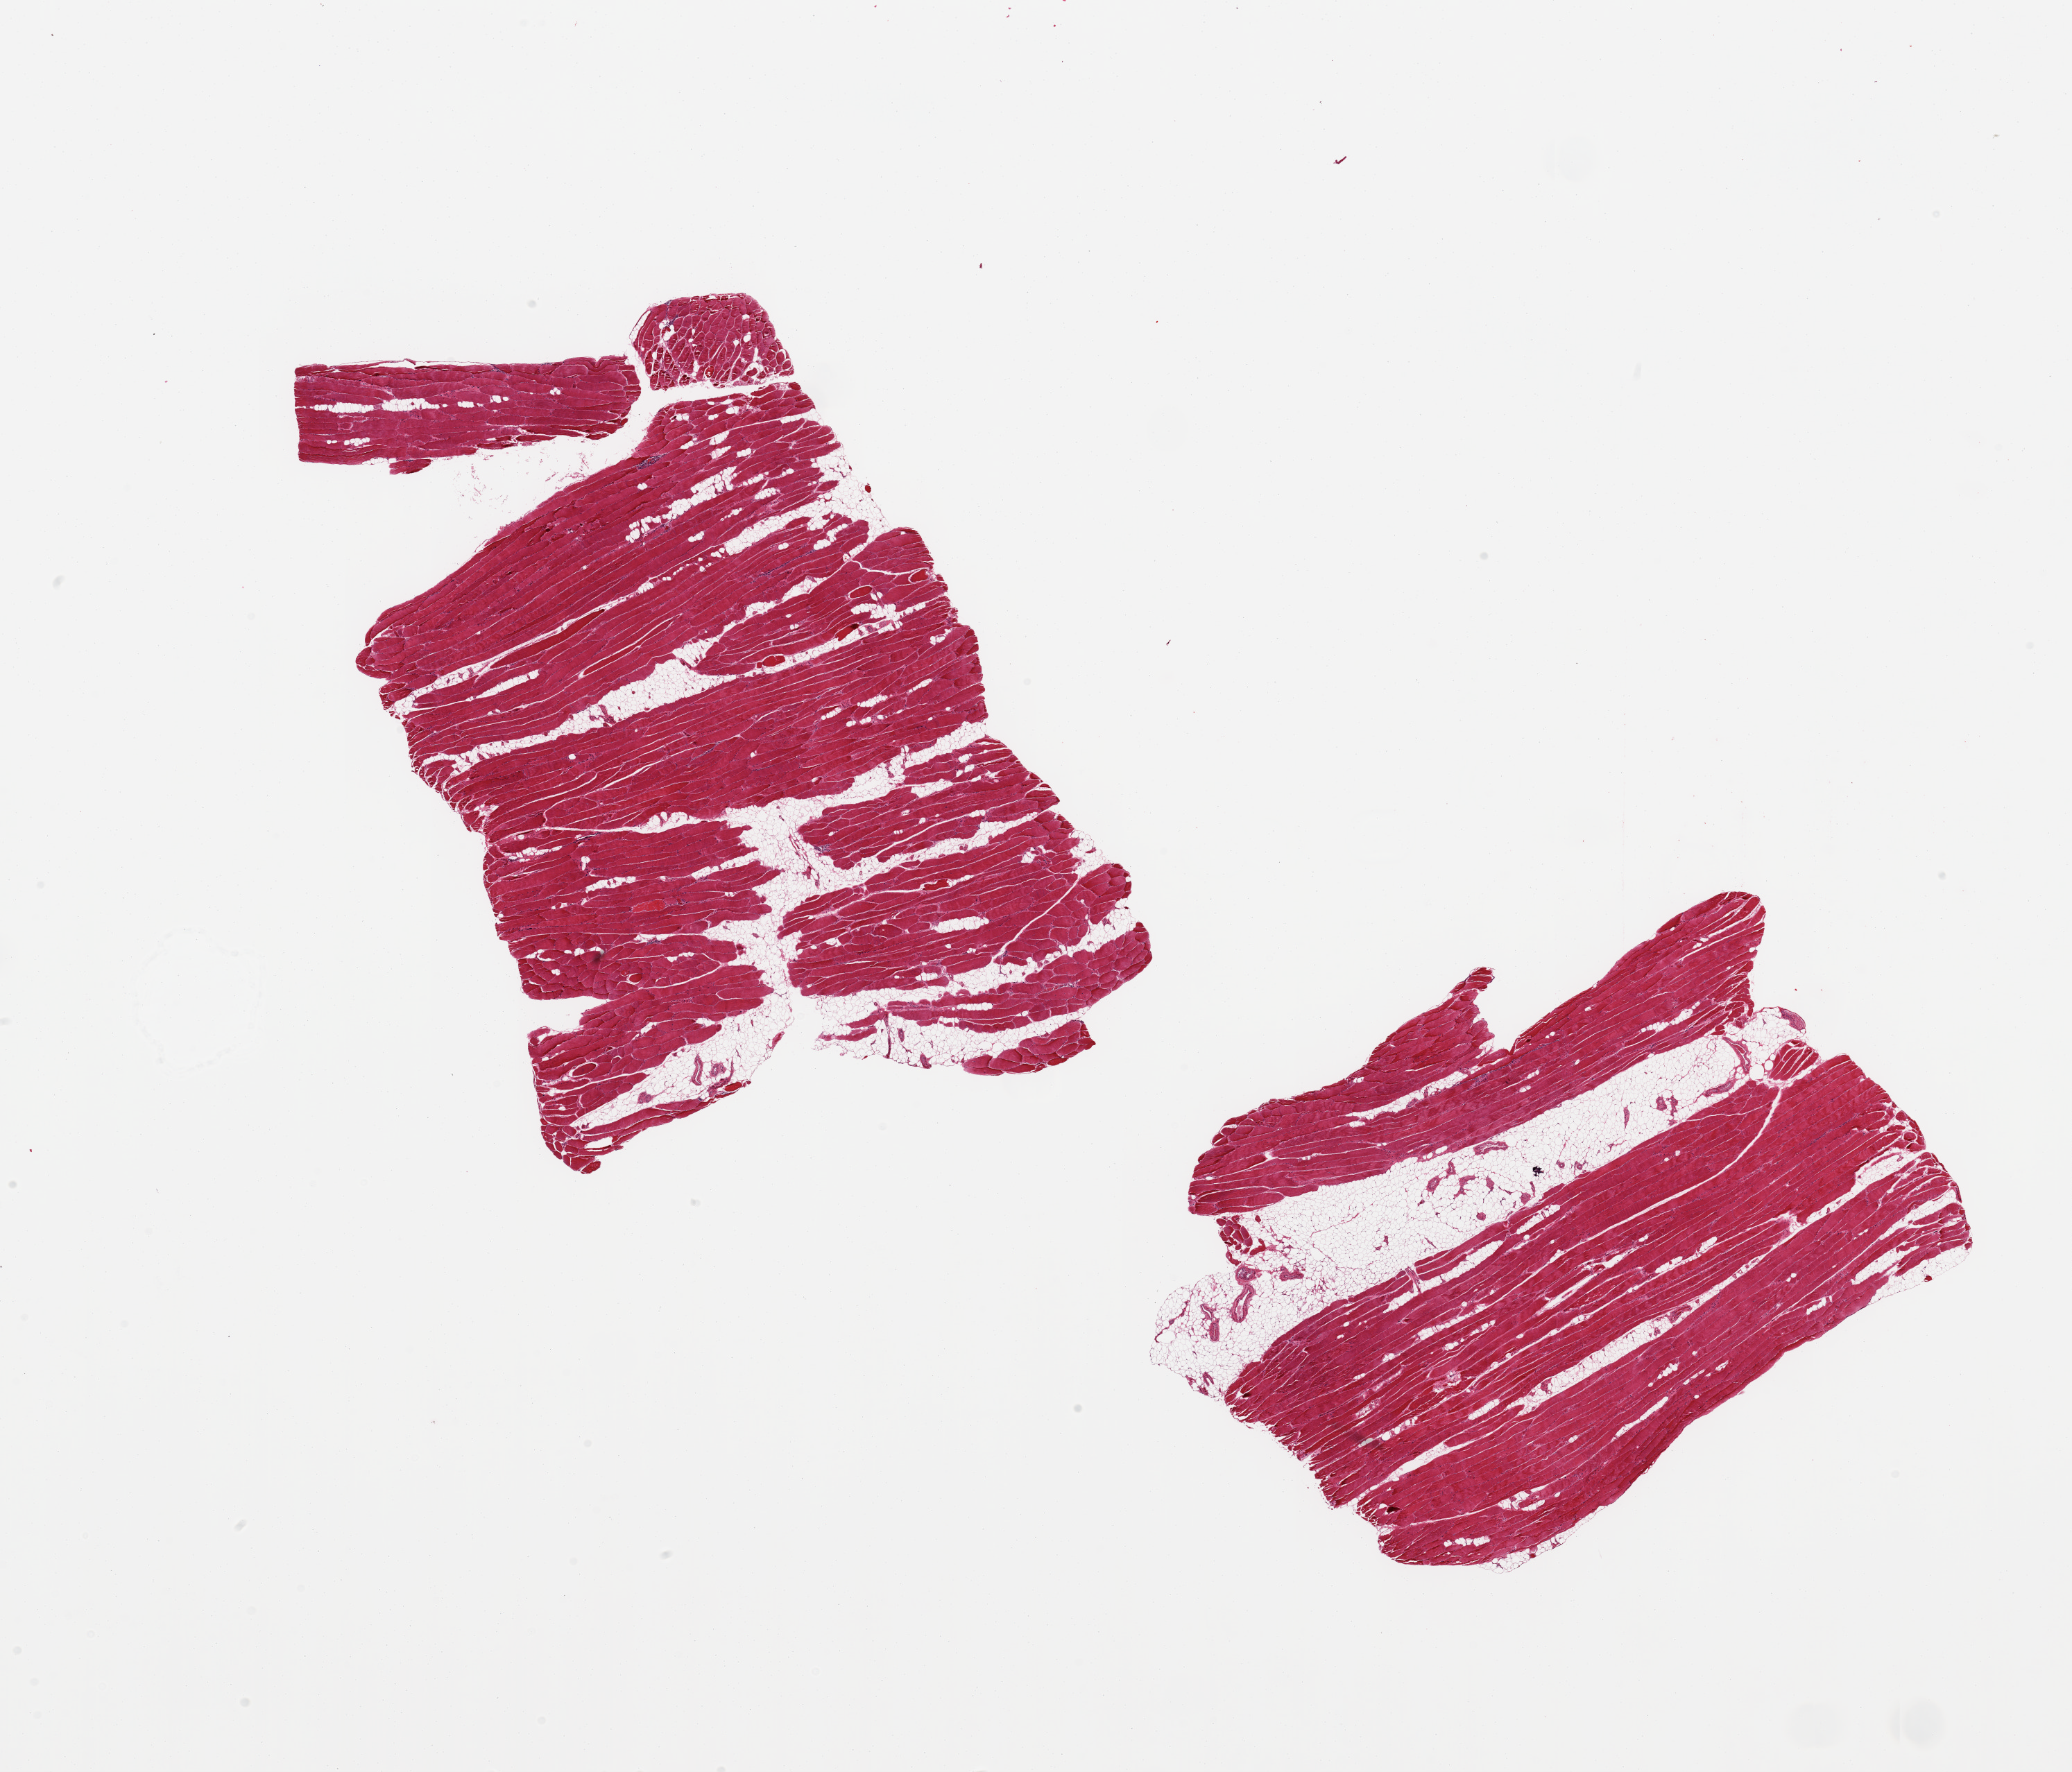
Hematoxylin and eosin (H&E) whole-slide image, brightfield — low-resolution overview of the scanned area, about 23.6 x 20.2 mm (from a 20x scan), PAXgene-fixed, paraffin-embedded tissue, sampled site (target tissue): skeletal muscle, donor tissue sample. Donor sex: female.
Pathologist's review note for this sample: 2 pieces; 20% internal fat.